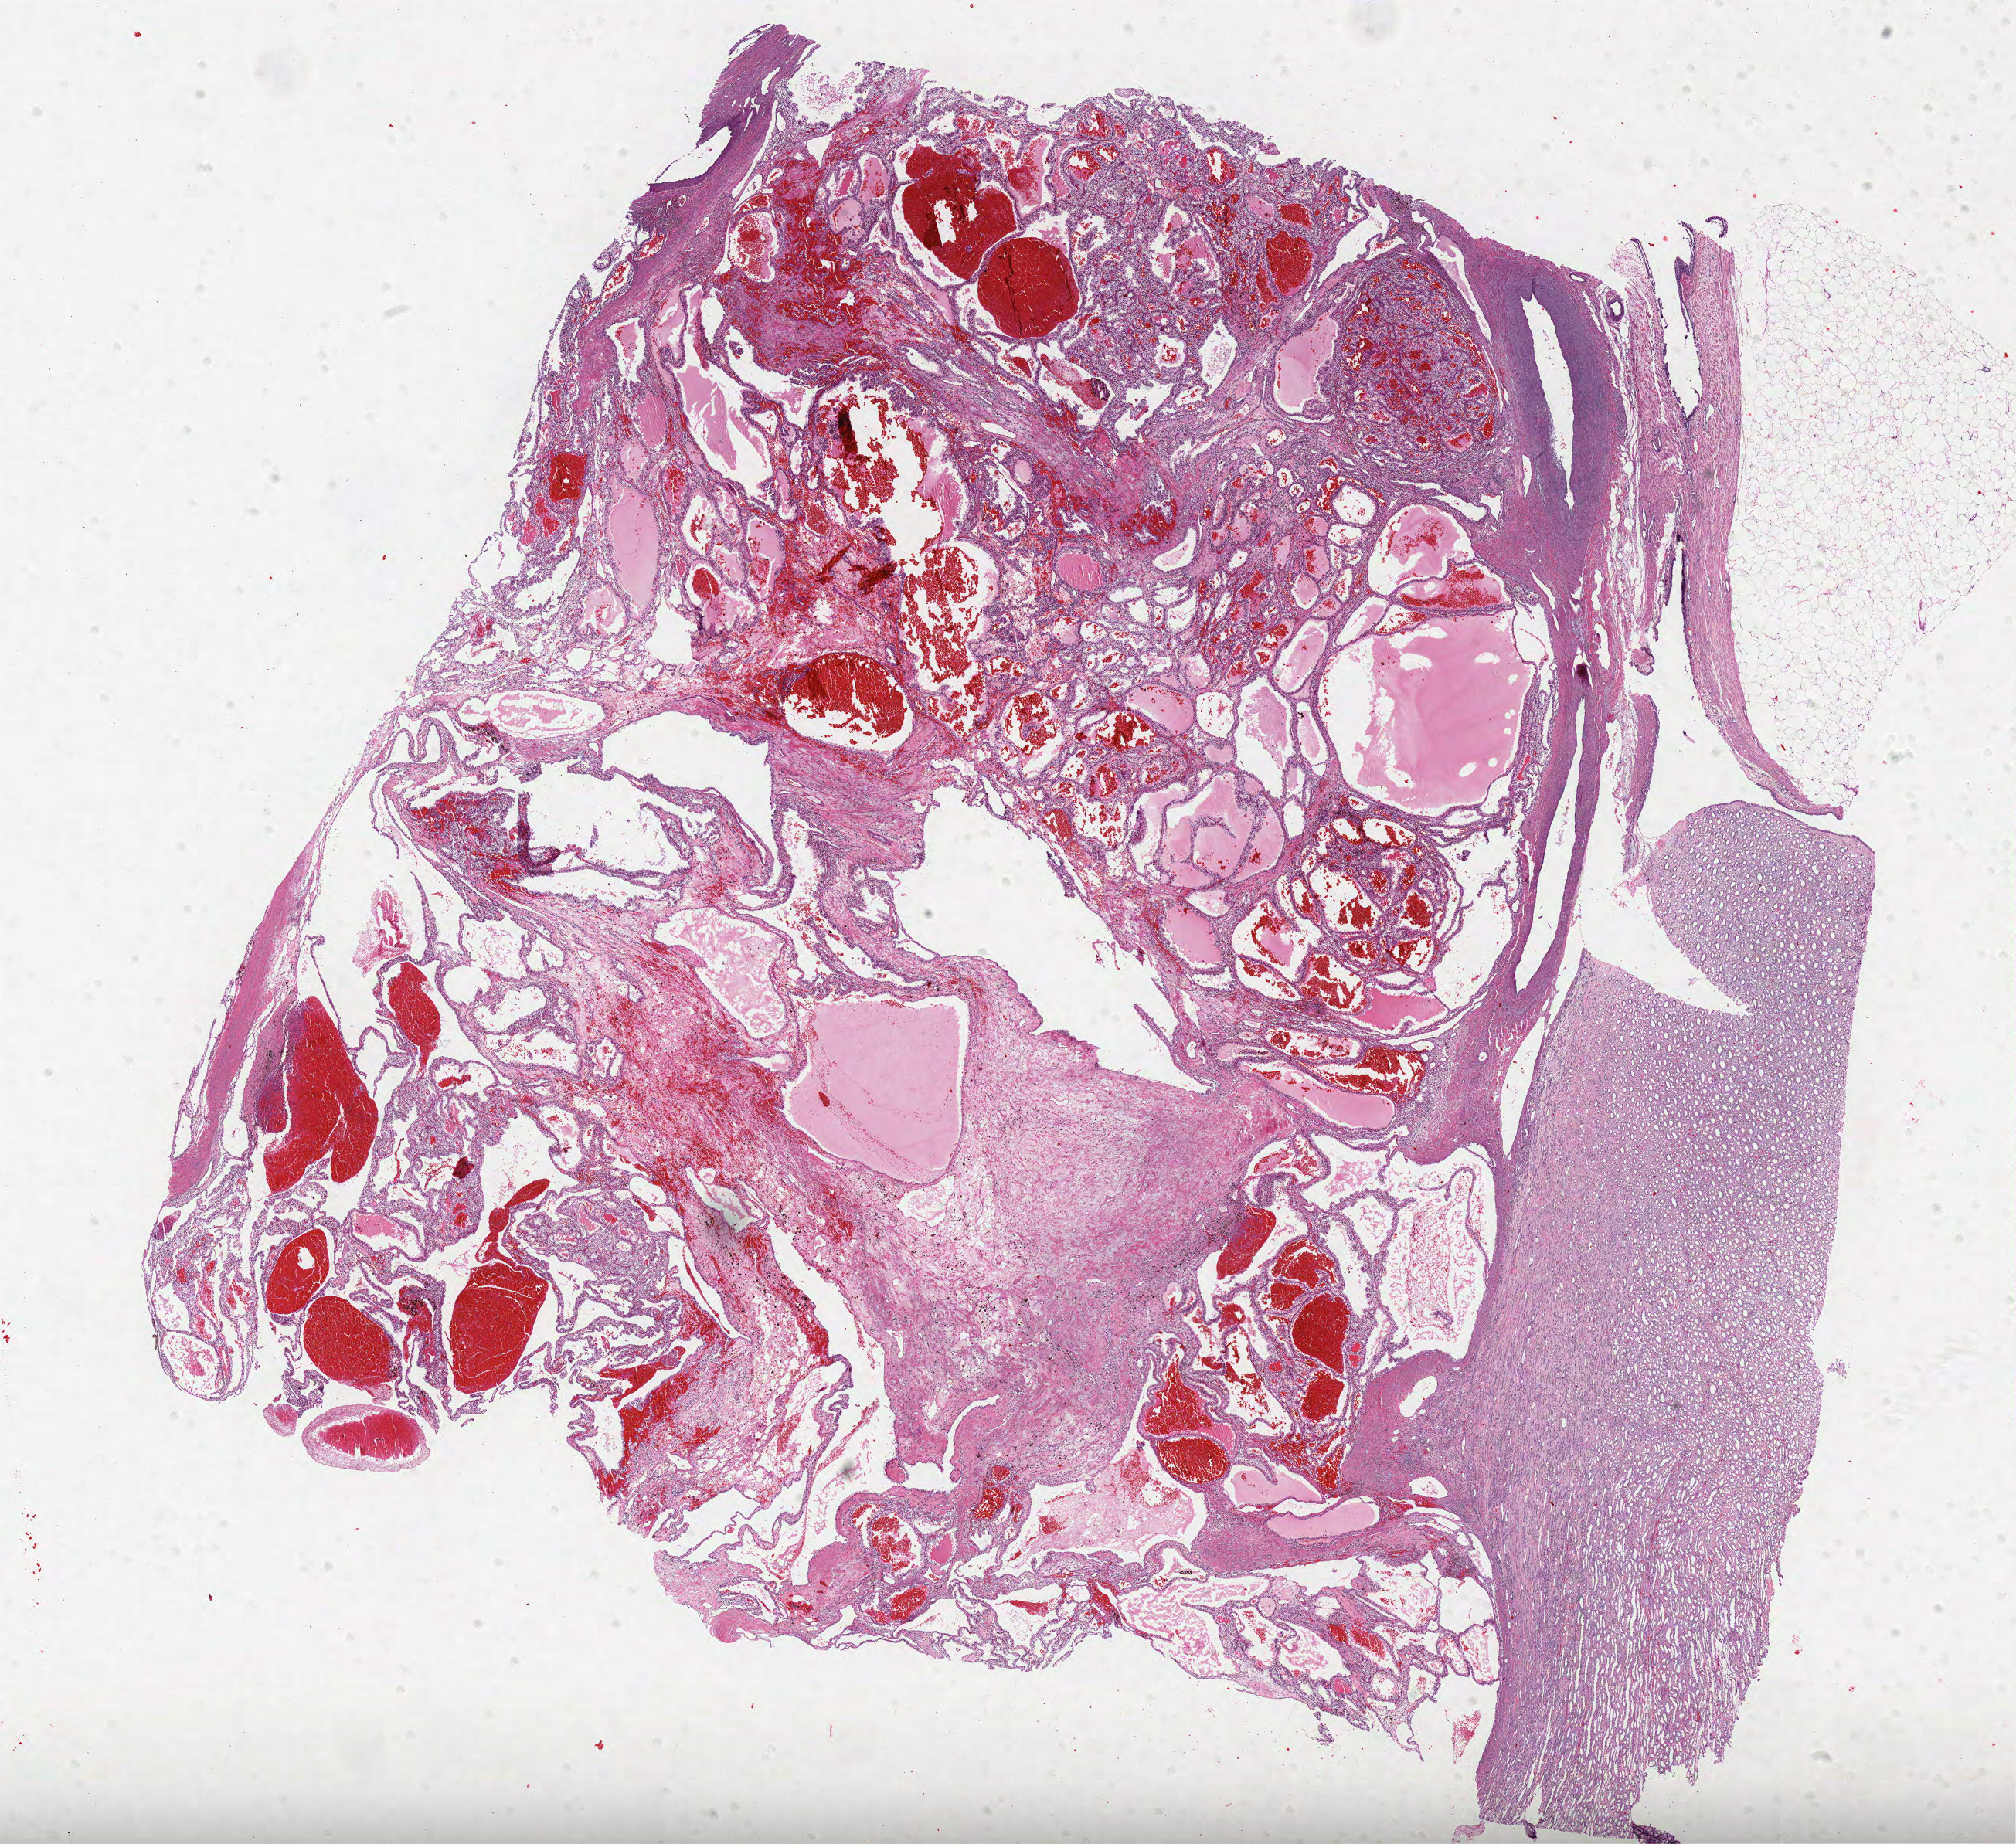
Whole-slide histology image, H&E, a low-resolution overview of the entire scanned area, about 20.9 x 19.1 mm, formalin-fixed paraffin-embedded (FFPE) diagnostic section, primary tumour sample from the kidney. Male, age 67 years at initial diagnosis. Histologic grade: G2 (moderately differentiated).
Diagnosis: Clear cell adenocarcinoma, NOS. Laterality: left. Lymph nodes positive (case pathology): 0 of 3 examined. AJCC pathologic stage: III.